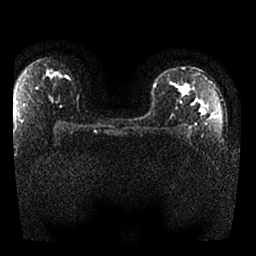
Breast MRI, one axial slice; position 18 of 25 along the scan axis; diffusion-weighted series; image 2 of 4 stored at this slice position (different b-values; order by instance number); 1.5 T; 256 × 256 image matrix, field of view 330 × 330 mm. Female patient.
Outlined on this slice (expert manual segmentation):
- tumour on diffusion-weighted imaging: bounding box <179,84,206,115> (left, top, right, bottom; pixels)